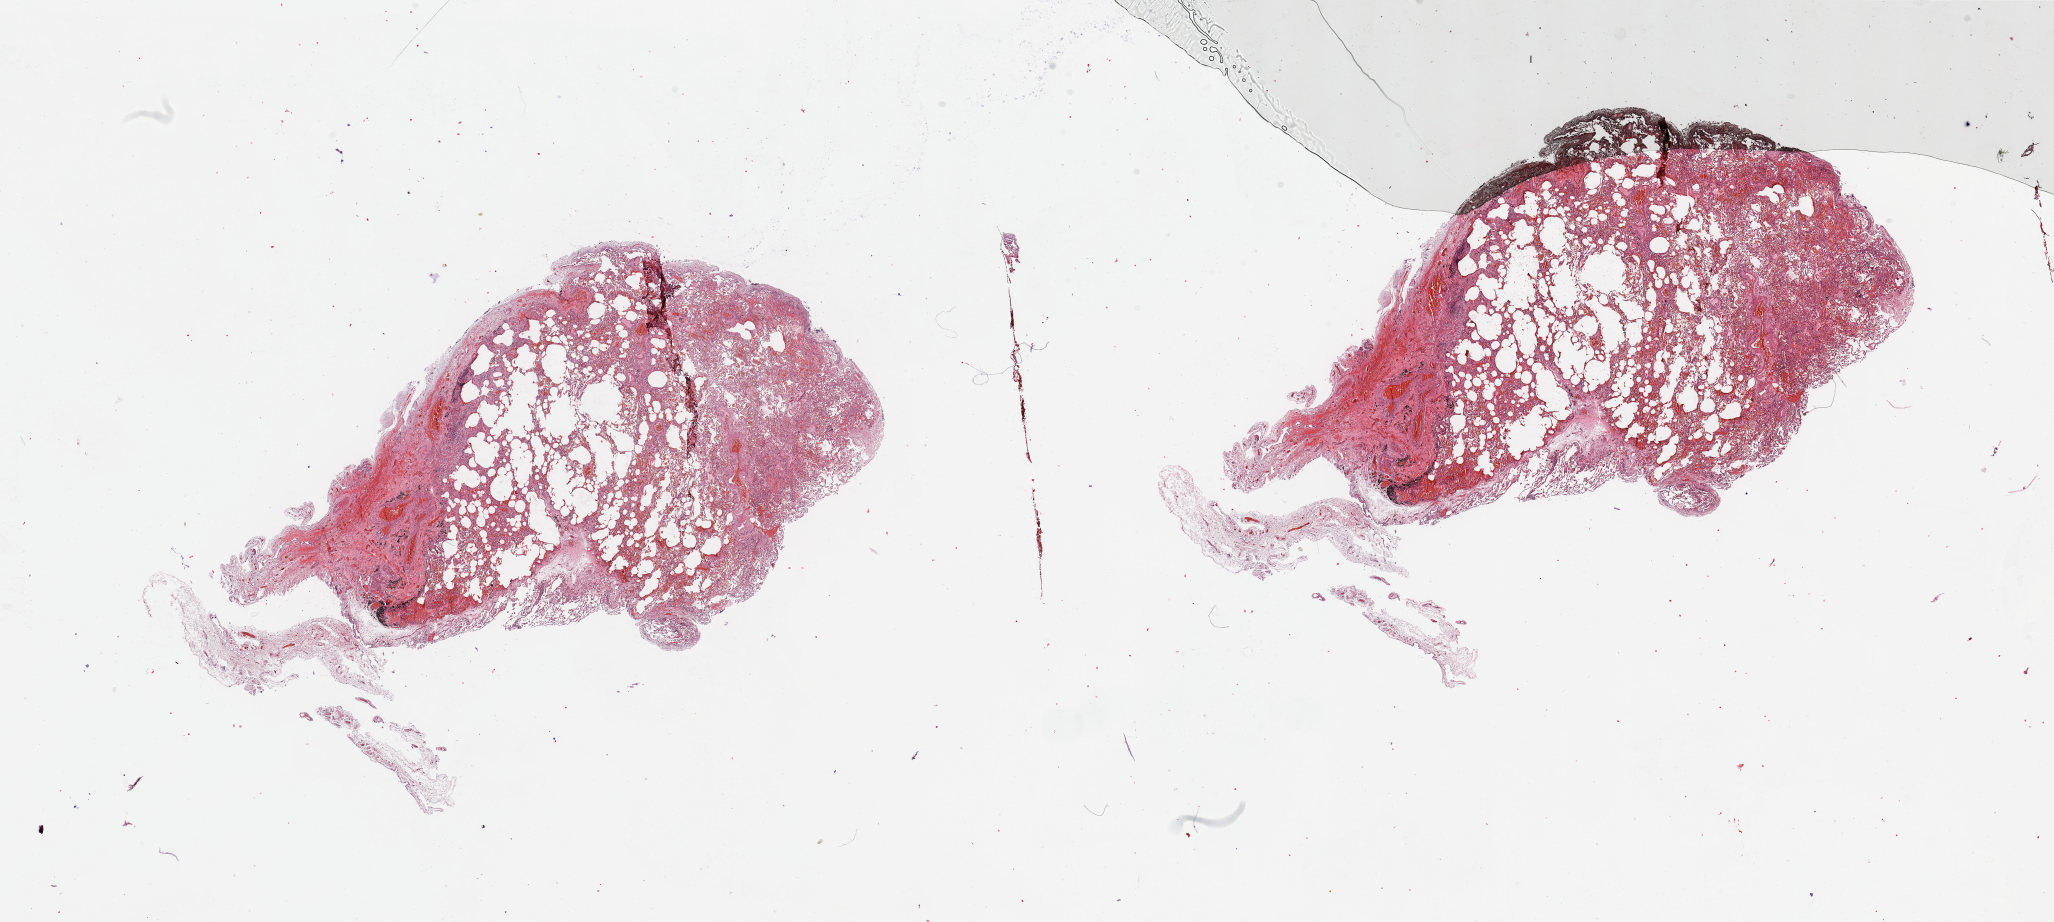
H&E-stained whole-slide image, a low-resolution overview of the entire scanned area, about 32.5 x 14.6 mm. Normal (non-tumour) tissue sample, sampled site: lung. Patient: male, age 61 years.
This section: normal (non-tumour) tissue from the same patient. Patient diagnosis: Squamous cell carcinoma, NOS.